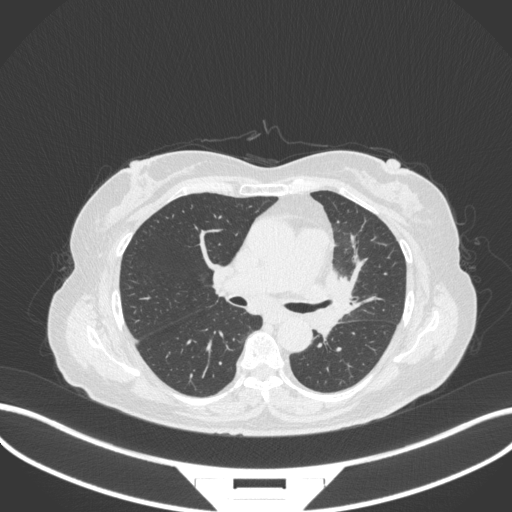
Chest CT, one axial slice; slice 193 of 382 in the series (ordered by position); reconstruction kernel B31f; 120 kVp; lung window (W 1500 / L -600 HU); 1 mm slice thickness; 512 × 512 image matrix. Female patient, age 64 years. Case-level facts recorded for this patient, not image findings: clinical TNM (as recorded): T2a N2 M0.
Outlined on this slice (bounding box drawn by a radiologist):
- lung tumour (recorded histology: adenocarcinoma): bounding box [x1, y1, x2, y2] px = [323, 264, 359, 344]